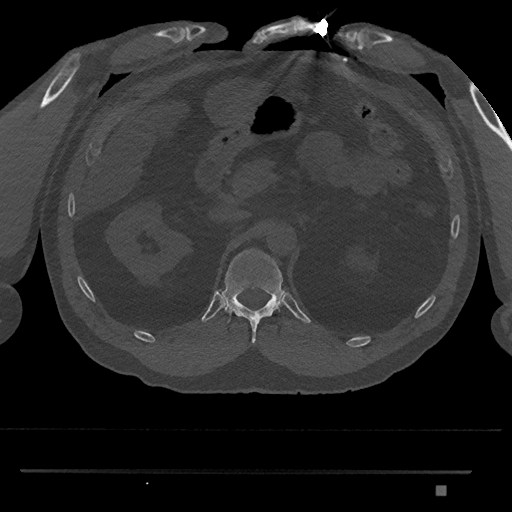
CT including the spine, one axial slice. Slice 884 of 1134 in the series (ordered by position). Reconstruction kernel Br40s/3. 120 kVp. Bone window (W 1800 / L 400 HU). 0.5 mm slice thickness. 512 × 512 image matrix. Patient: male, 65 years. From the clinical record (not read from this slice): primary cancer: prostate.
Annotated regions visible in this slice (semi-automatic segmentation, software-assisted and operator-edited):
- T12 vertebra: bounding box <219,249,285,344> (left, top, right, bottom; pixels)